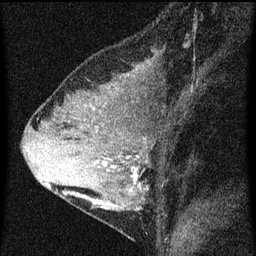
Breast MRI (dynamic contrast-enhanced), one sagittal slice; slice 29 of 60 in the series (ordered by position); dynamic contrast-enhanced series, image 2 of 3 at this slice position (ordered by acquisition); 1.5 T; TE 4.2 ms, TR 8 ms; 2 mm slice thickness; 256 × 256 image matrix, field of view 180 × 180 mm. Female patient, age 33 years.
Structures marked on this image (semi-automatically segmented with operator editing):
- analysis volume of interest (the breast-tissue region the enhancement analysis was run in; not a lesion): bounding box (x1, y1, x2, y2) in pixels: (67, 118, 157, 215)
- tumour enhancement mask (voxels above the 70 % enhancement threshold inside the analysis volume of interest): (93, 152, 141, 209)